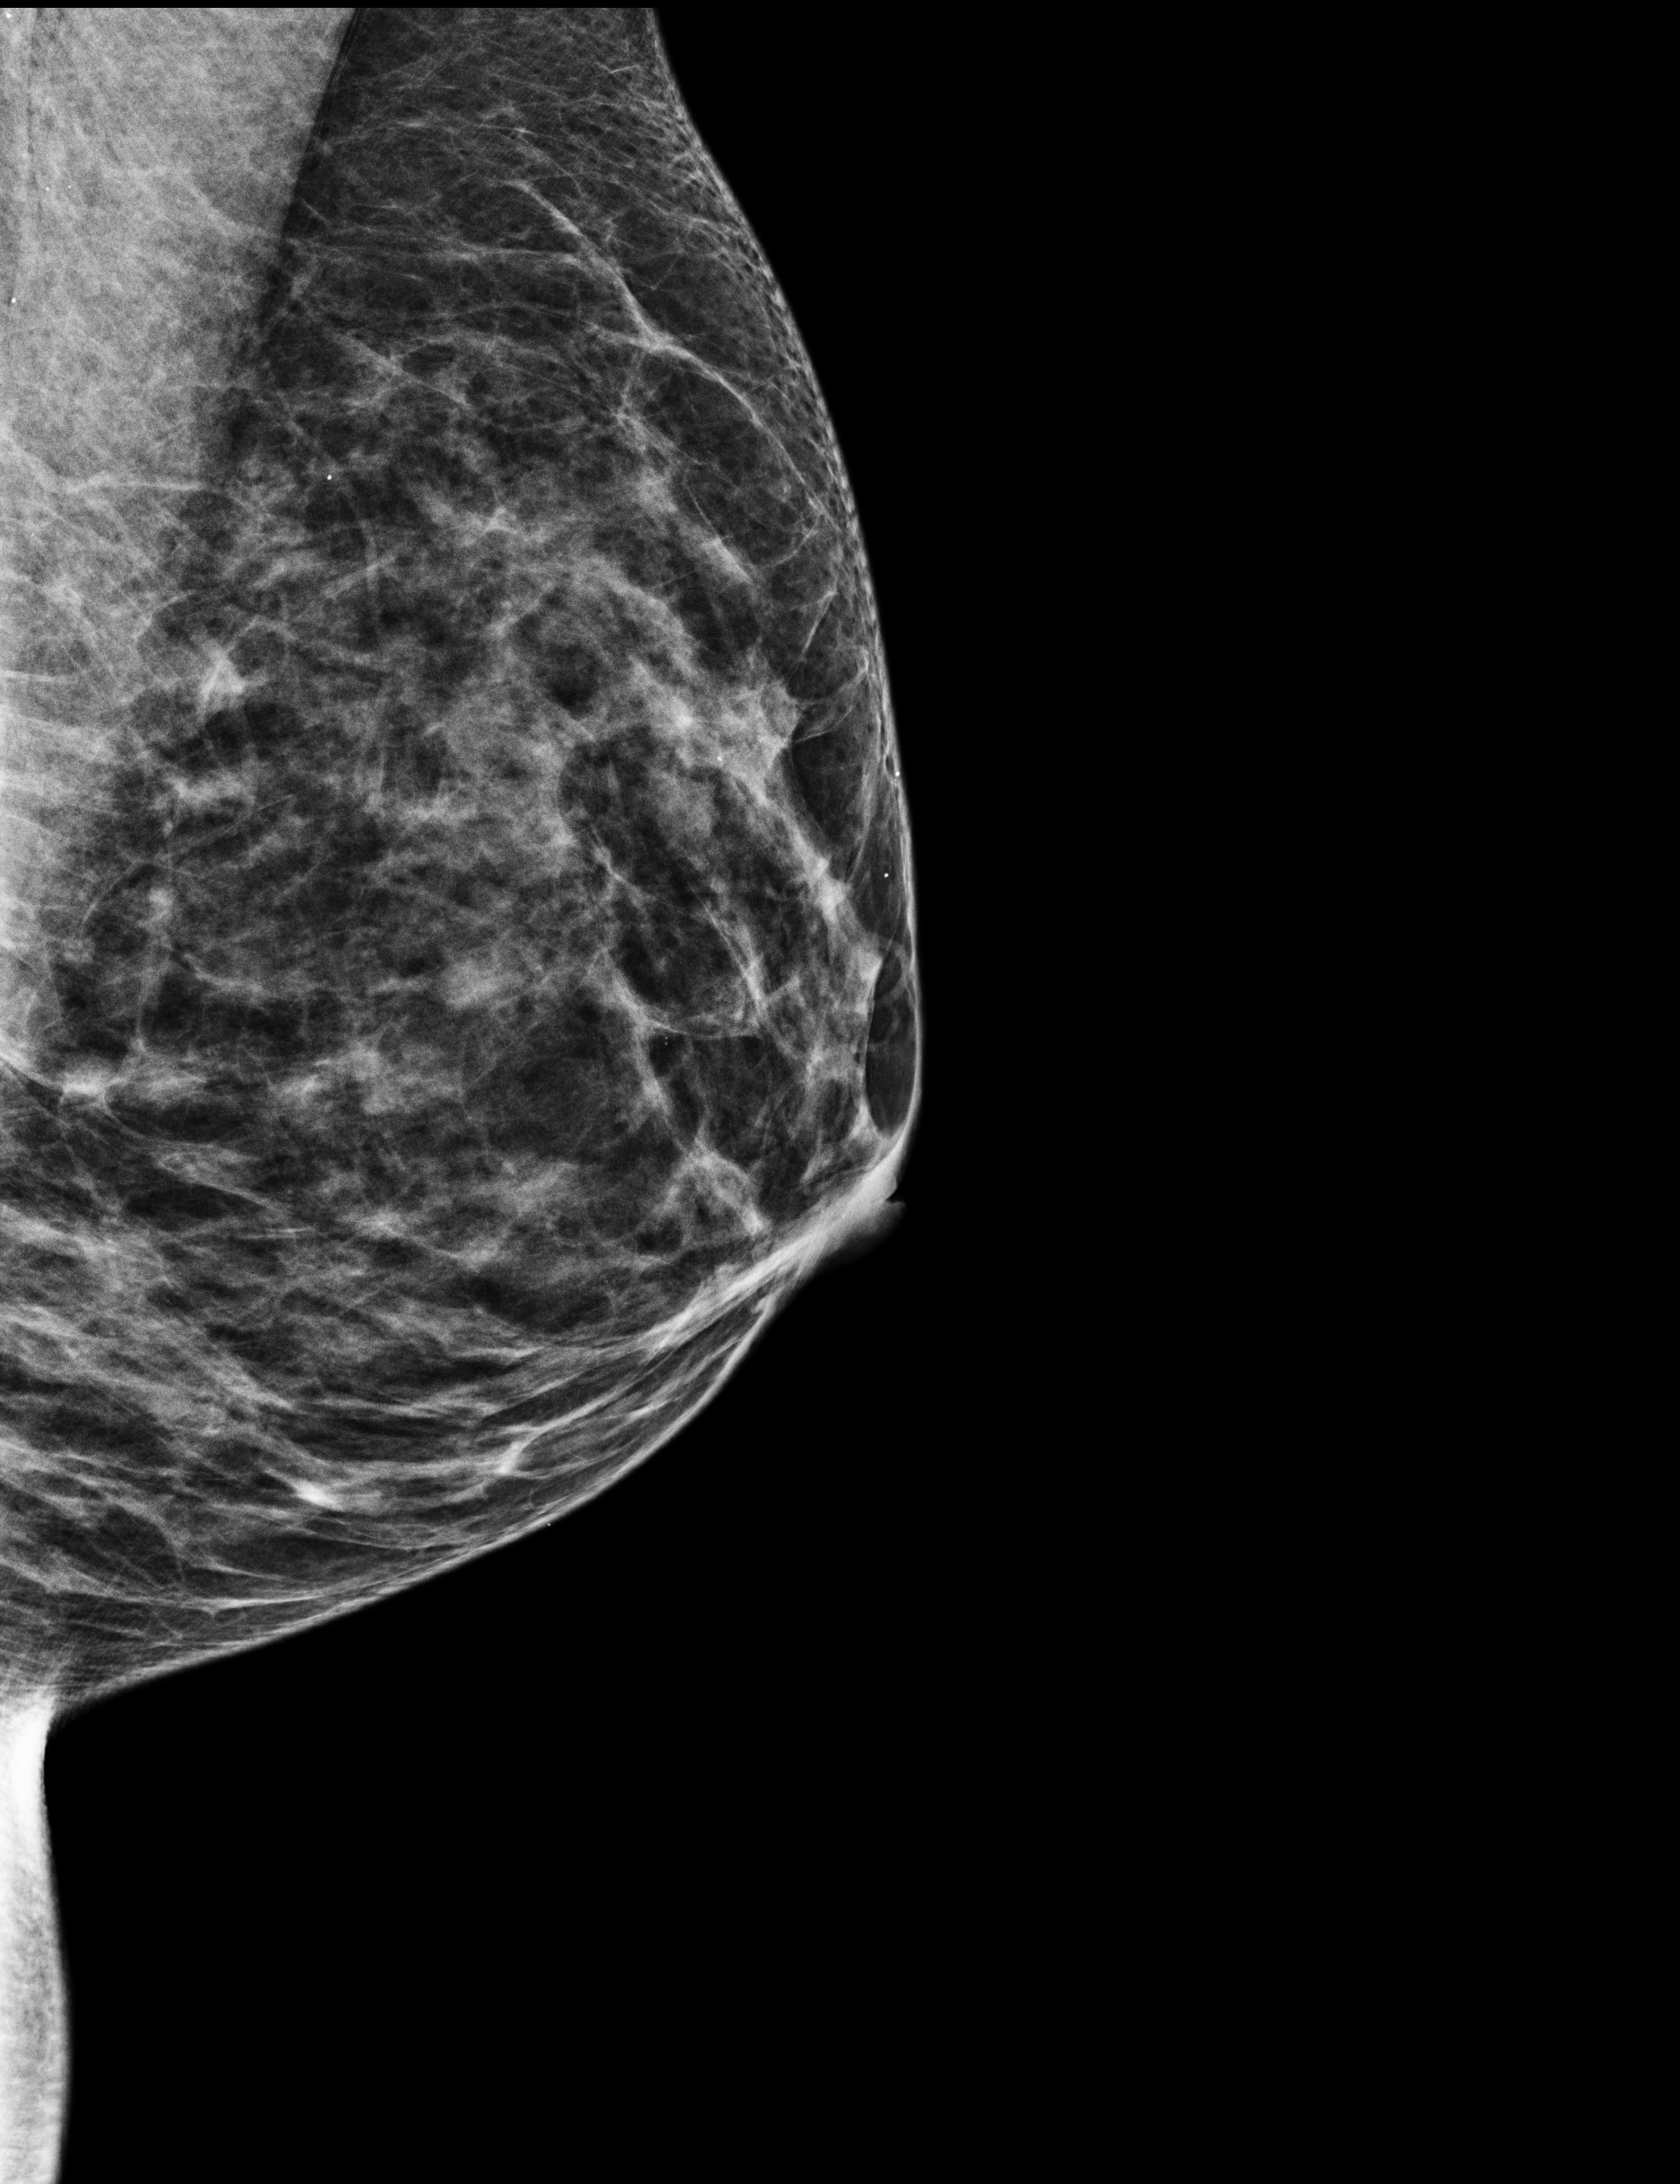
Screening examination, compressed breast thickness 41 mm, system: Selenia Dimensions. Female patient, age 44 years.
Image type: full-field digital mammogram. Breast: left. Projection: medio-lateral oblique projection.